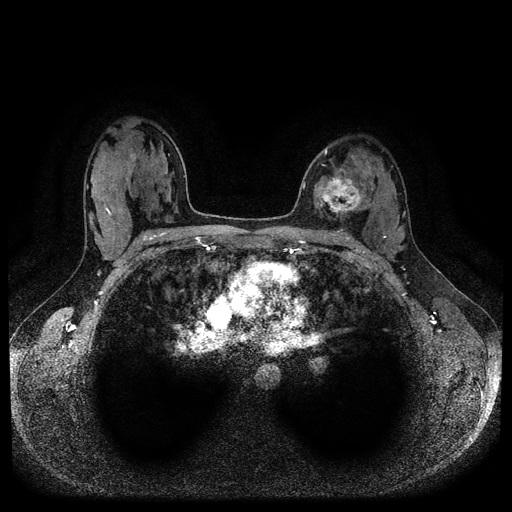
Breast MRI (dynamic contrast-enhanced, multi-phase), one axial slice. Slice 63 of 116 in the series (ordered by position). Dynamic contrast-enhanced series, time point 2 of 5 at this slice position (early post-contrast). 1.5 T. TE 2.6 ms, TR 5.3 ms. 2 mm slice thickness. 512 × 512 image matrix, field of view 350 × 350 mm. Female patient, age 33 years.
Annotated regions visible in this slice (semi-automatic segmentation, software-assisted and operator-edited):
- breast lesion (labelled 'tumour' in the annotation; benign lesions carry a separate 'benign' label): bounding box (x1, y1, x2, y2) in pixels: (315, 171, 364, 218)